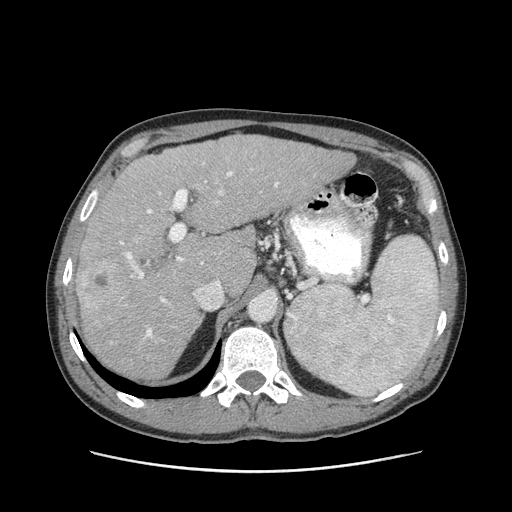
Contrast-enhanced abdominal CT (liver protocol), one axial slice. Position 64 of 93 along the scan axis. Reconstruction kernel STANDARD. Soft-tissue window (W 400 / L 40 HU). 2.5 mm slice thickness. 512 × 512 image matrix. From the clinical record (not read from this slice): diagnosis: hepatocellular carcinoma (patient treated with transarterial chemoembolisation; whether this scan precedes or follows treatment is not stated here); TNM stage (as recorded): Stage-II; Child-Pugh class: A; tumour nodularity: multinodular; tumour size: 1 cm.
Structures marked on this image (semi-automatic segmentation, software-assisted and operator-edited):
- liver parenchyma outside the tumour (the mass and vessels are separate outlines, so this box may not span the whole liver): bounding box <76,134,354,380> (left, top, right, bottom; pixels)
- mass: <80,259,128,310>
- liver vessels: <120,171,278,338>